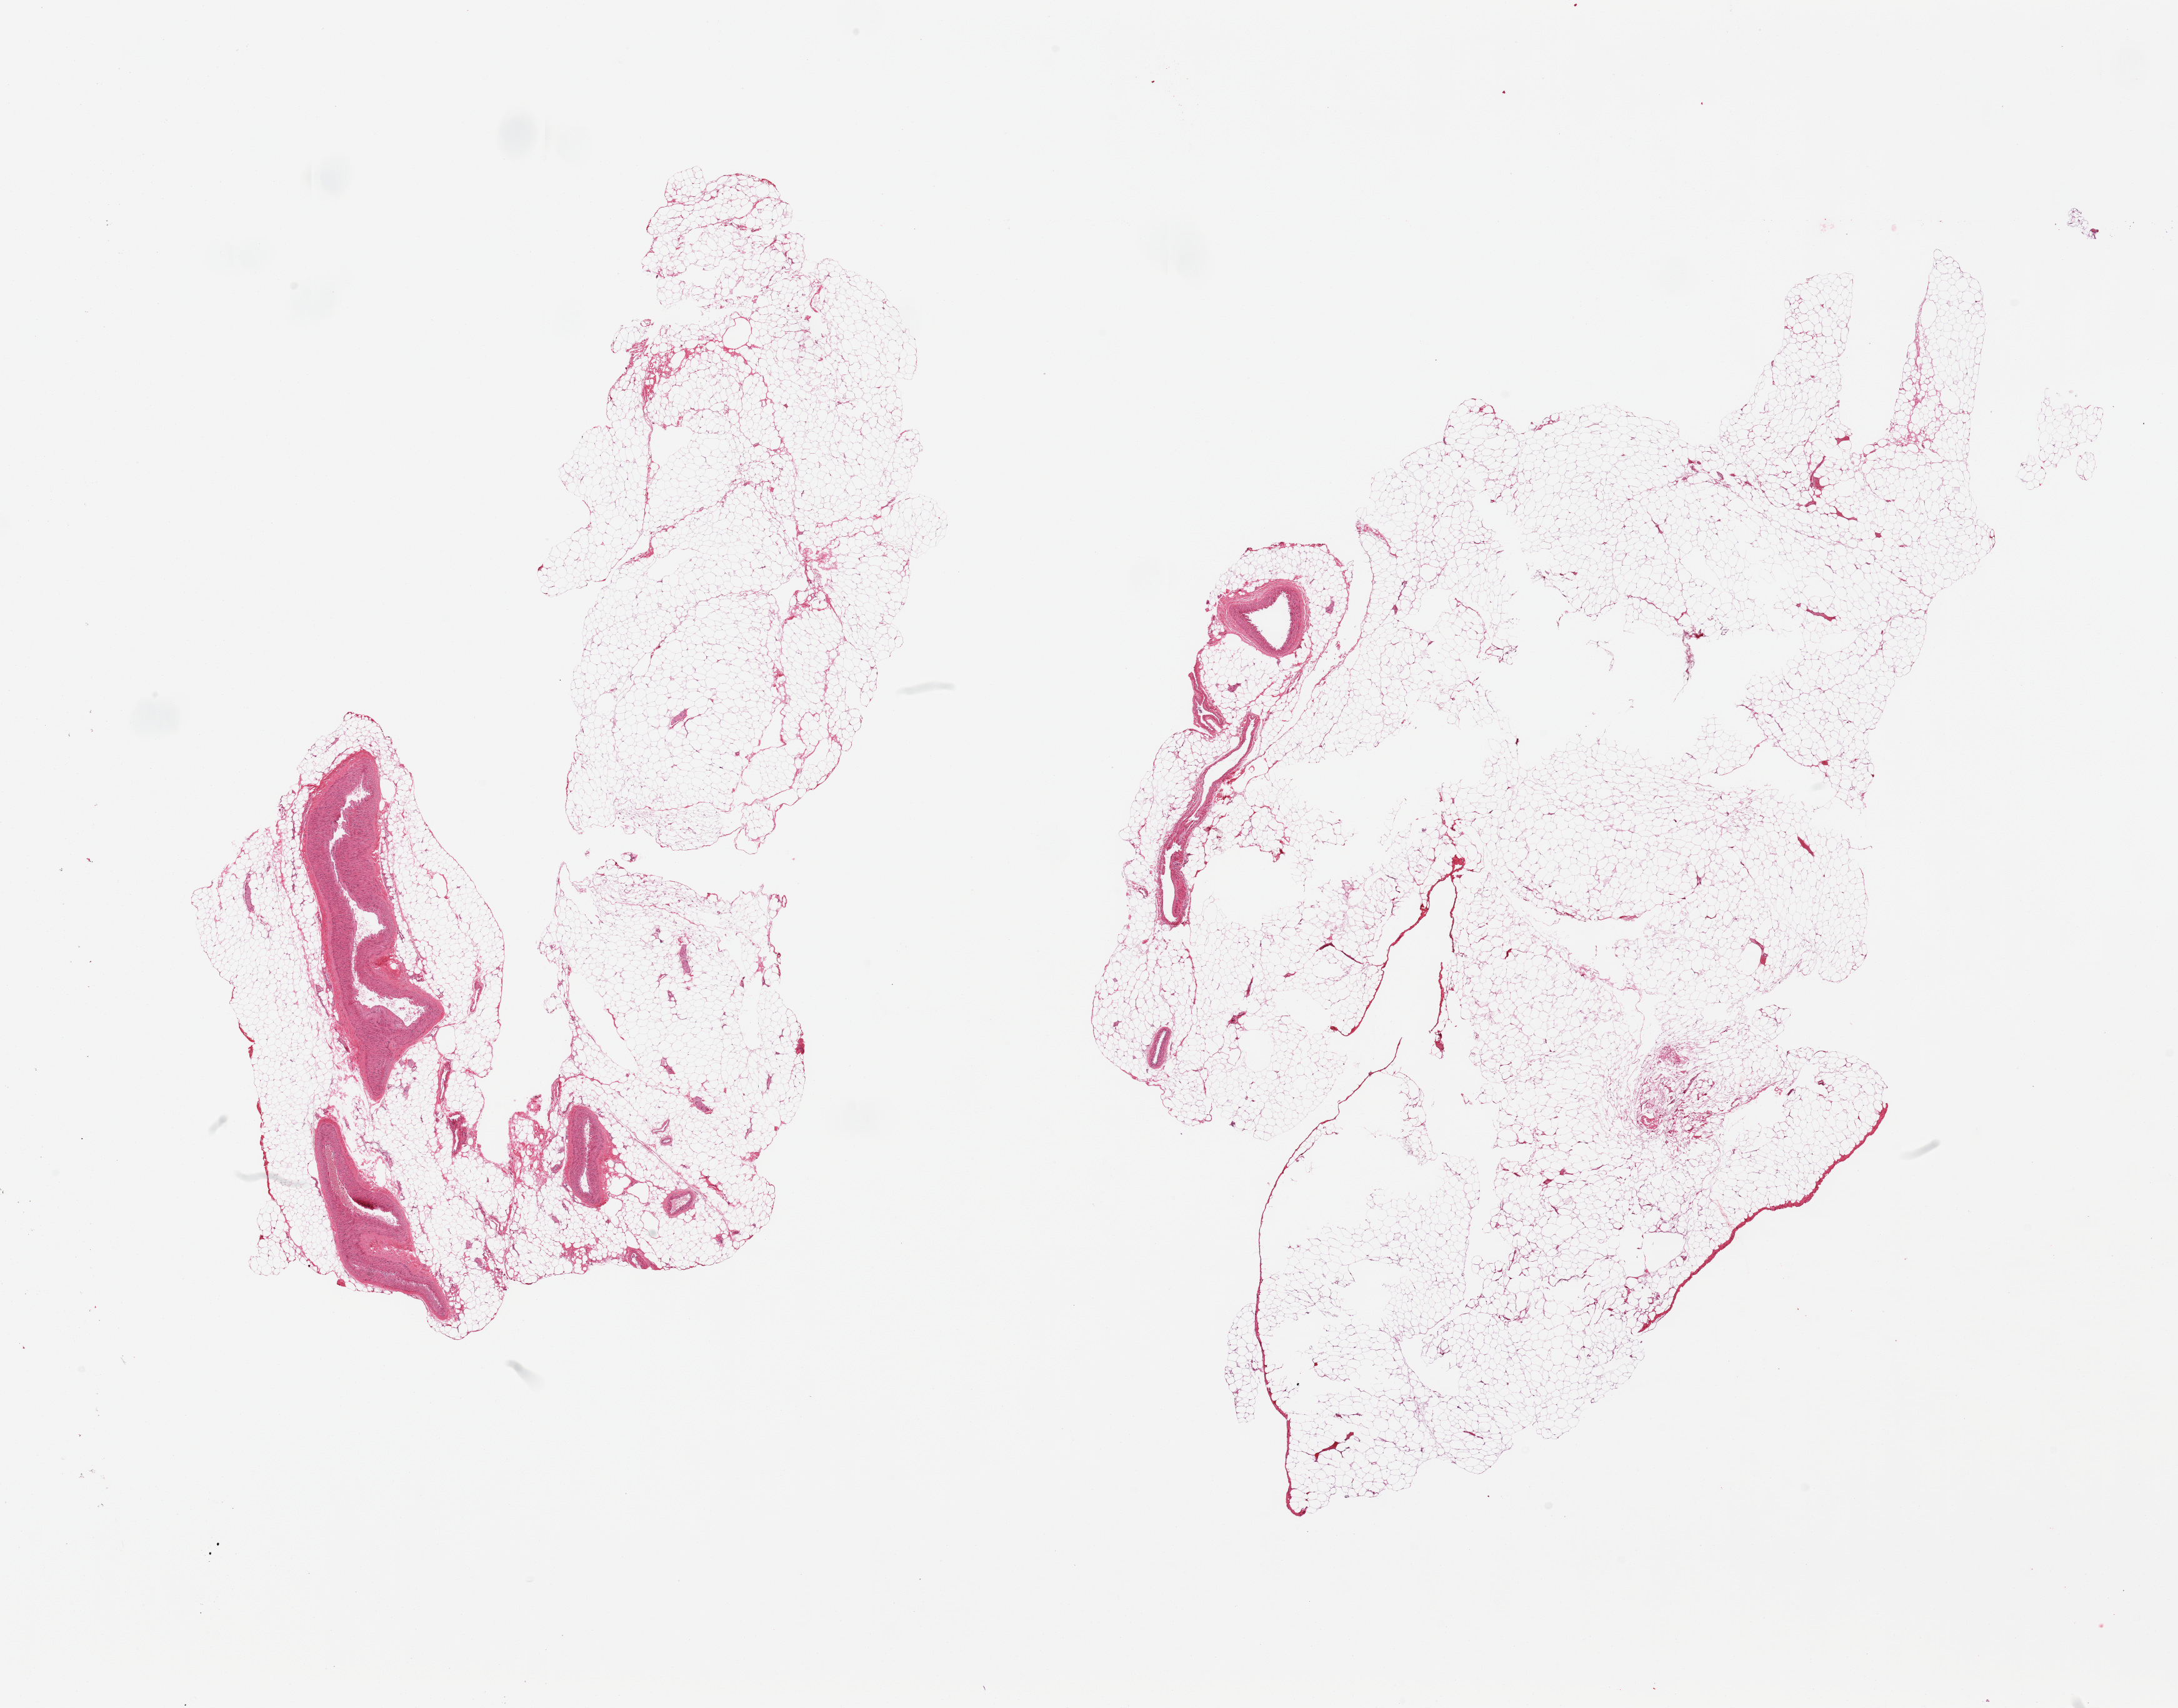
Digitized hematoxylin and eosin (H&E)-stained section, shown as a low-resolution overview of the whole scanned area (about 27.6 x 21.6 mm). PAXgene-fixed, paraffin-embedded tissue. Sampled site (target tissue): omentum. Tissue donor sample. Donor: male.
* pathologist's review note for this sample: 2 pieces; contains several prominent arteries